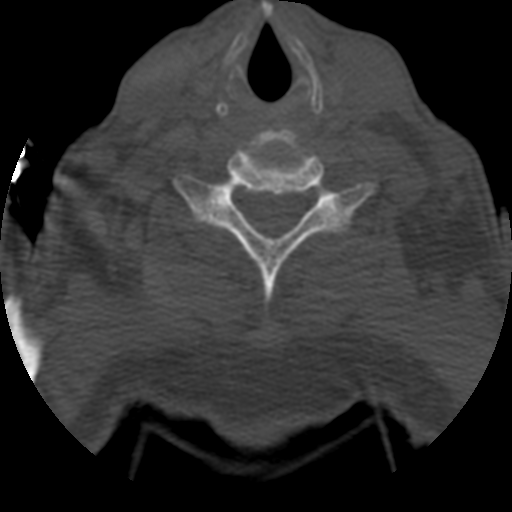
CT including the spine, one axial slice. Position 533 of 708 along the scan axis. One of 3 acquisitions stored at this slice position. Bone window (W 1800 / L 400 HU). 512 × 512 image matrix, field of view 160 × 160 mm. Patient age 55 years. From the clinical record (not read from this slice): primary cancer: colon; vertebrae with lytic lesions (as recorded): T12, L1, L5.
Outlined on this slice (semi-automatic segmentation, software-assisted and operator-edited):
- T1 vertebra: bounding box <227,200,242,219> (left, top, right, bottom; pixels)